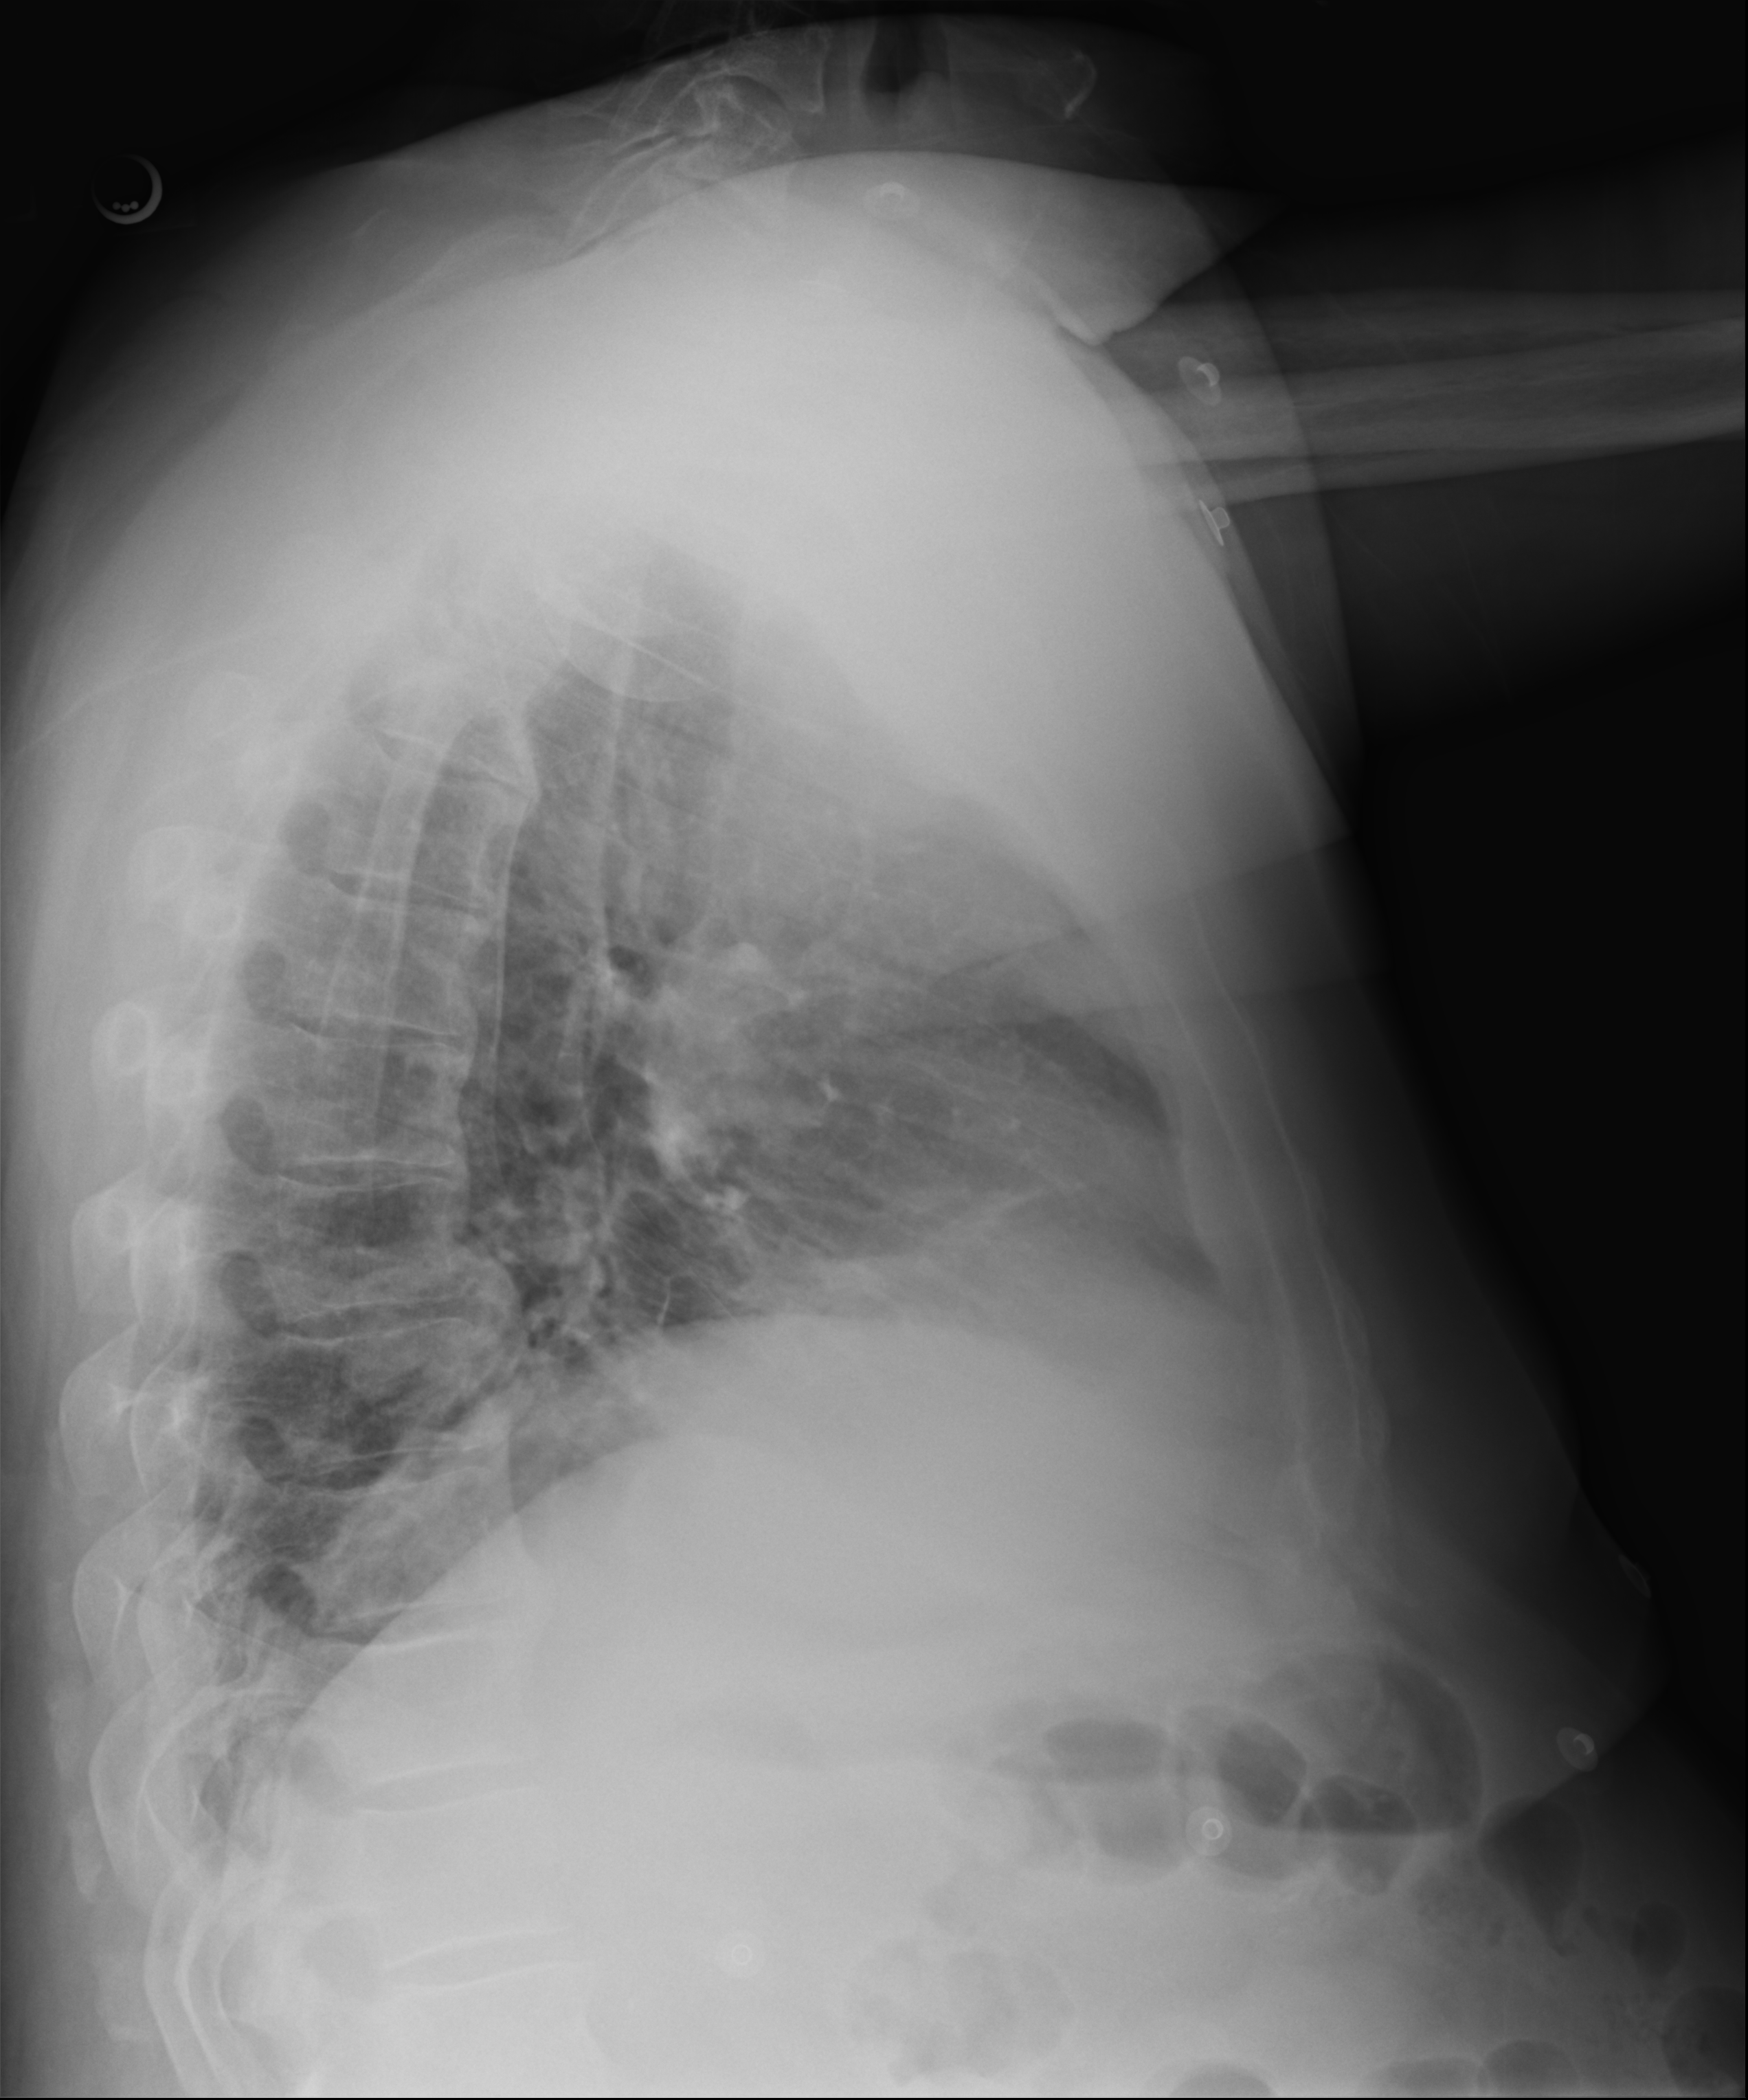
Chest X-ray, lateral projection. Male patient hospitalised with COVID-19, age 60–74 years.
Admission-level facts for this patient (not findings on this image; timing relative to this image not recorded): mechanically ventilated during this hospital stay: no.